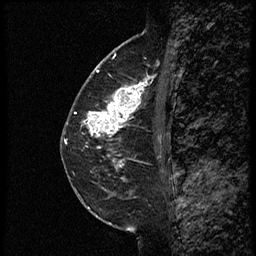
Breast MRI (dynamic contrast-enhanced), one sagittal slice; position 33 of 60 along the scan axis; dynamic contrast-enhanced study with each time point stored as its own series, time point 2 of 3 at this slice position (early post-contrast, ordered by acquisition time); 1.5 T; TE 4.2 ms, TR 18.9 ms; 2 mm slice thickness; 256 × 256 image matrix. Female patient. From the clinical record (not read from this slice): setting: breast cancer imaged before/during neoadjuvant chemotherapy; receptor status: HER2-positive.
Structures marked on this image (semi-automatically segmented with operator editing):
- analysis volume of interest (the breast-tissue region the enhancement analysis was run in; not a lesion): box from (x=85, y=74) to (x=161, y=147) px
- tumour enhancement mask (voxels above the 100 % enhancement threshold inside the analysis volume of interest): (x=89, y=75)–(x=151, y=139)